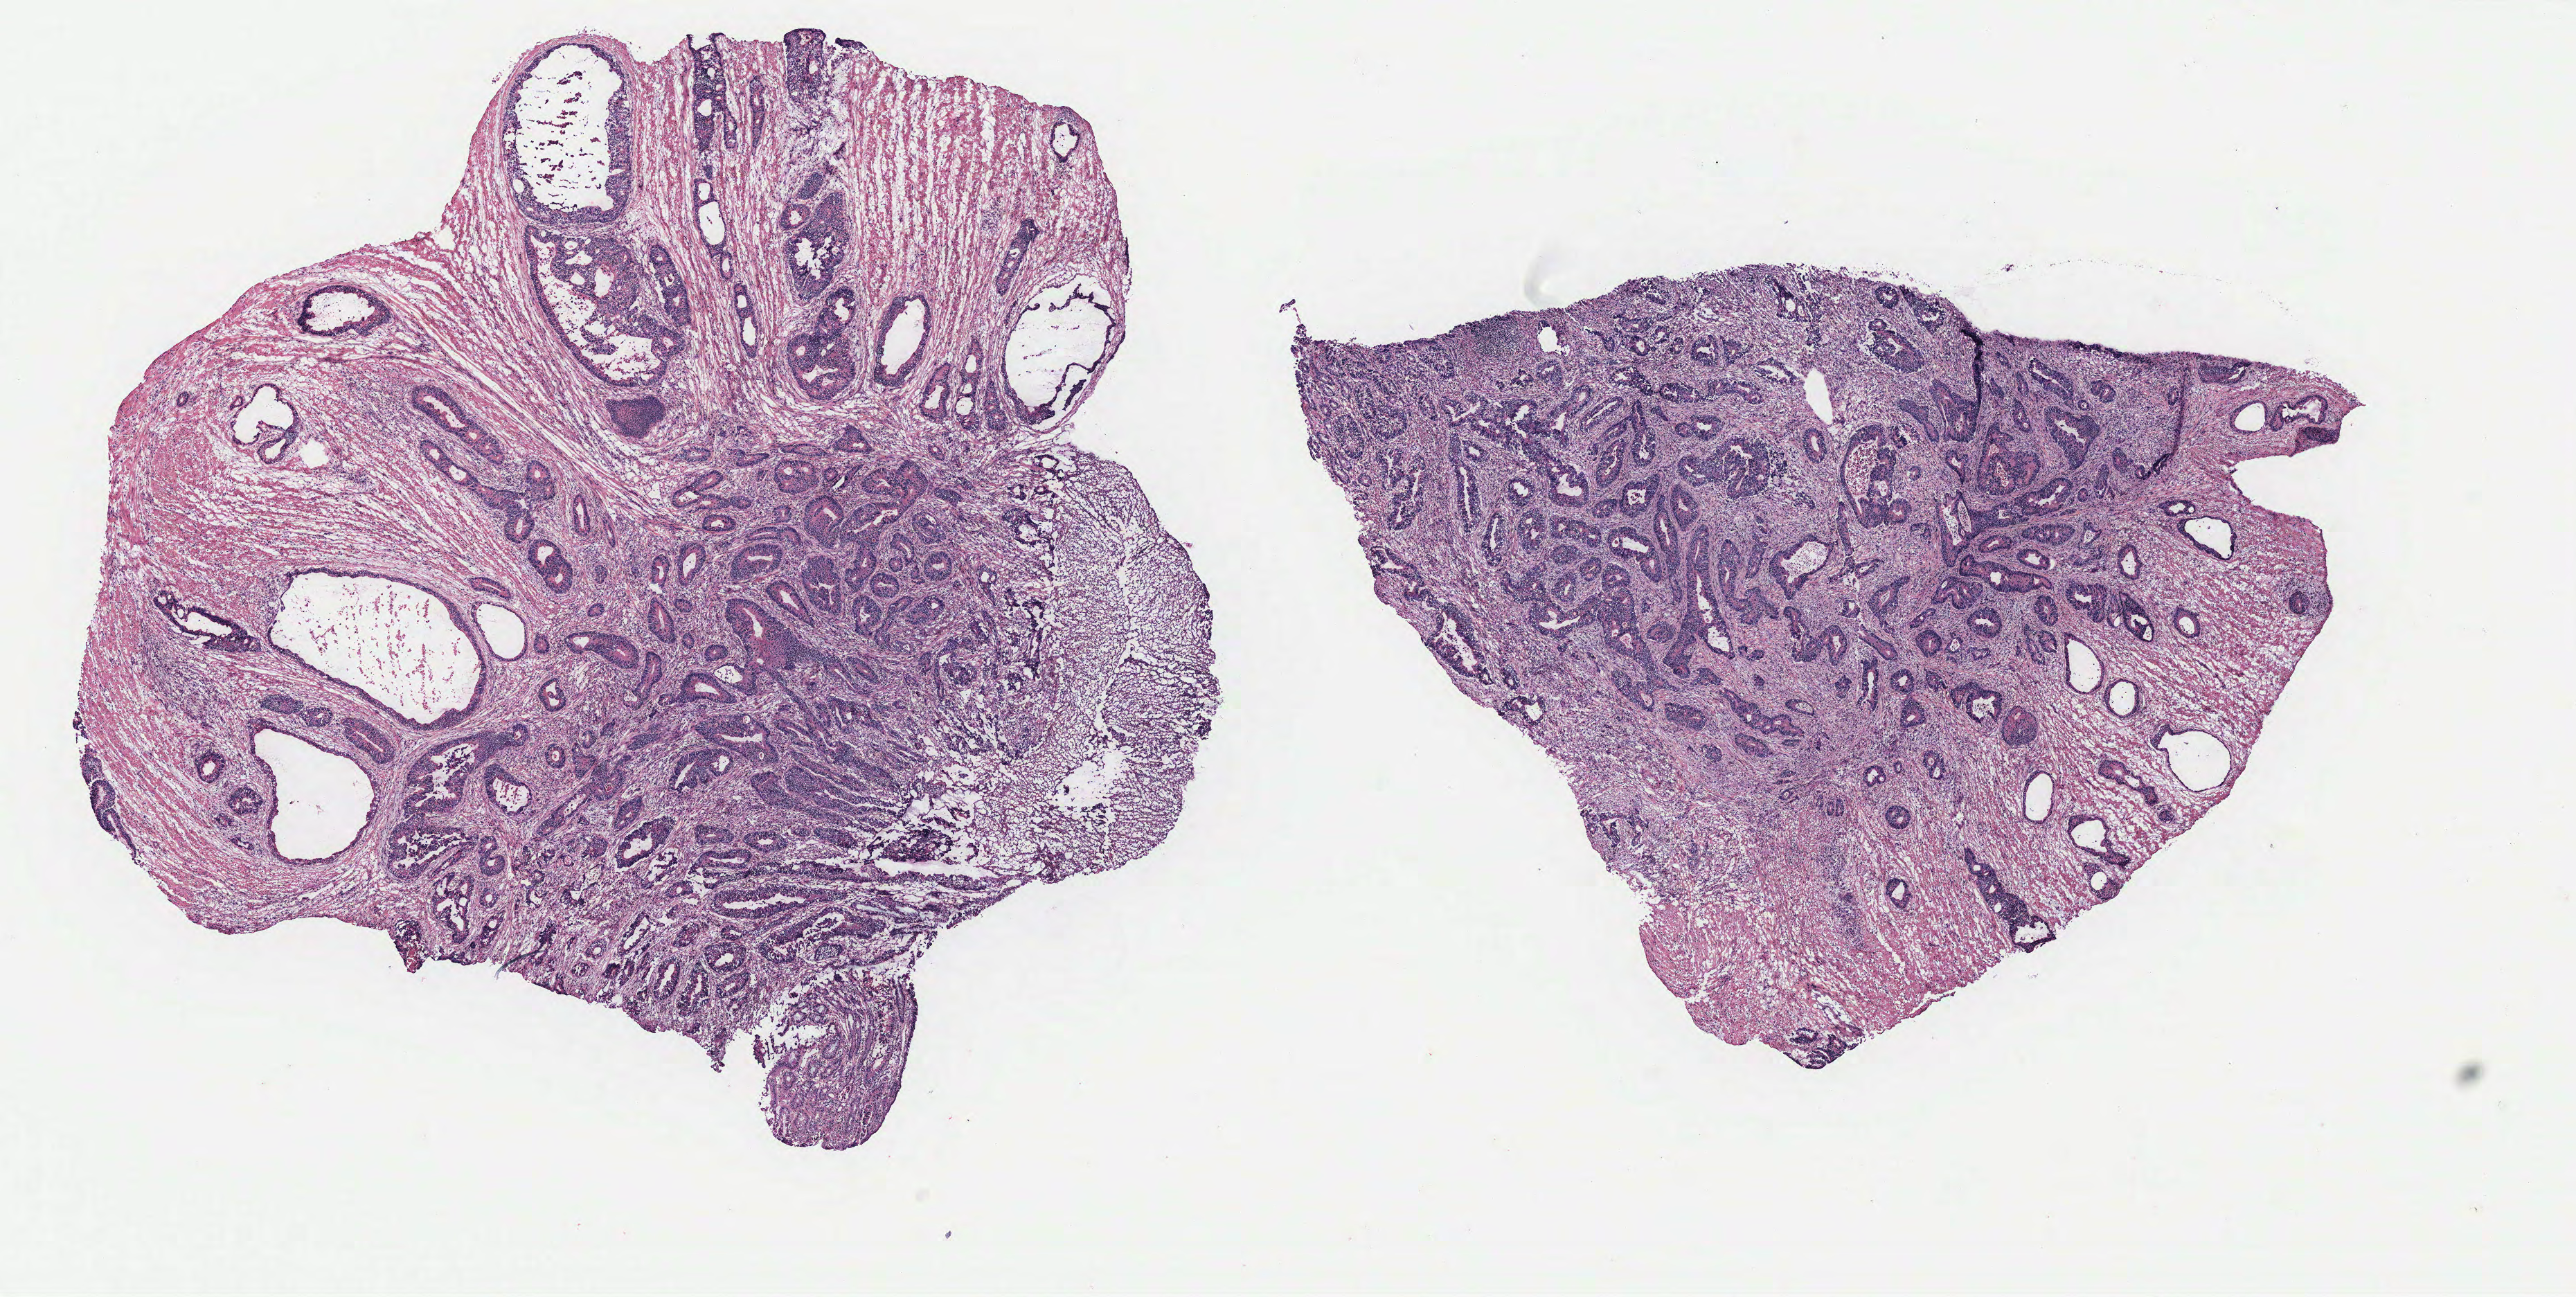
H&E whole-slide image — low-resolution overview of the scanned area, about 14.9 x 7.5 mm; colon, tissue type not recorded.
Patient diagnosis (cohort enrolment): colon cancer (colon).